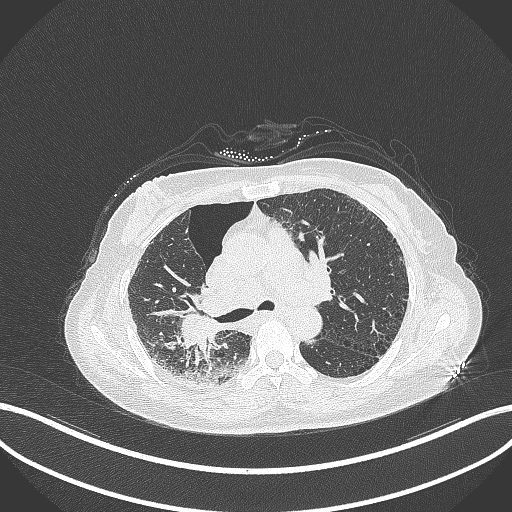
Chest CT, one axial slice; position 215 of 408 along the scan axis; lung window (W 1500 / L -600 HU); 1 mm slice thickness; 512 × 512 image matrix, field of view 400 × 400 mm. Female patient, age 64 years. From the clinical record (not read from this slice): clinical TNM (as recorded): T3 N3 M0.
Outlined on this slice (bounding box drawn by a radiologist):
- lung tumour (recorded histology: squamous cell carcinoma): box from (x=173, y=303) to (x=229, y=356) px